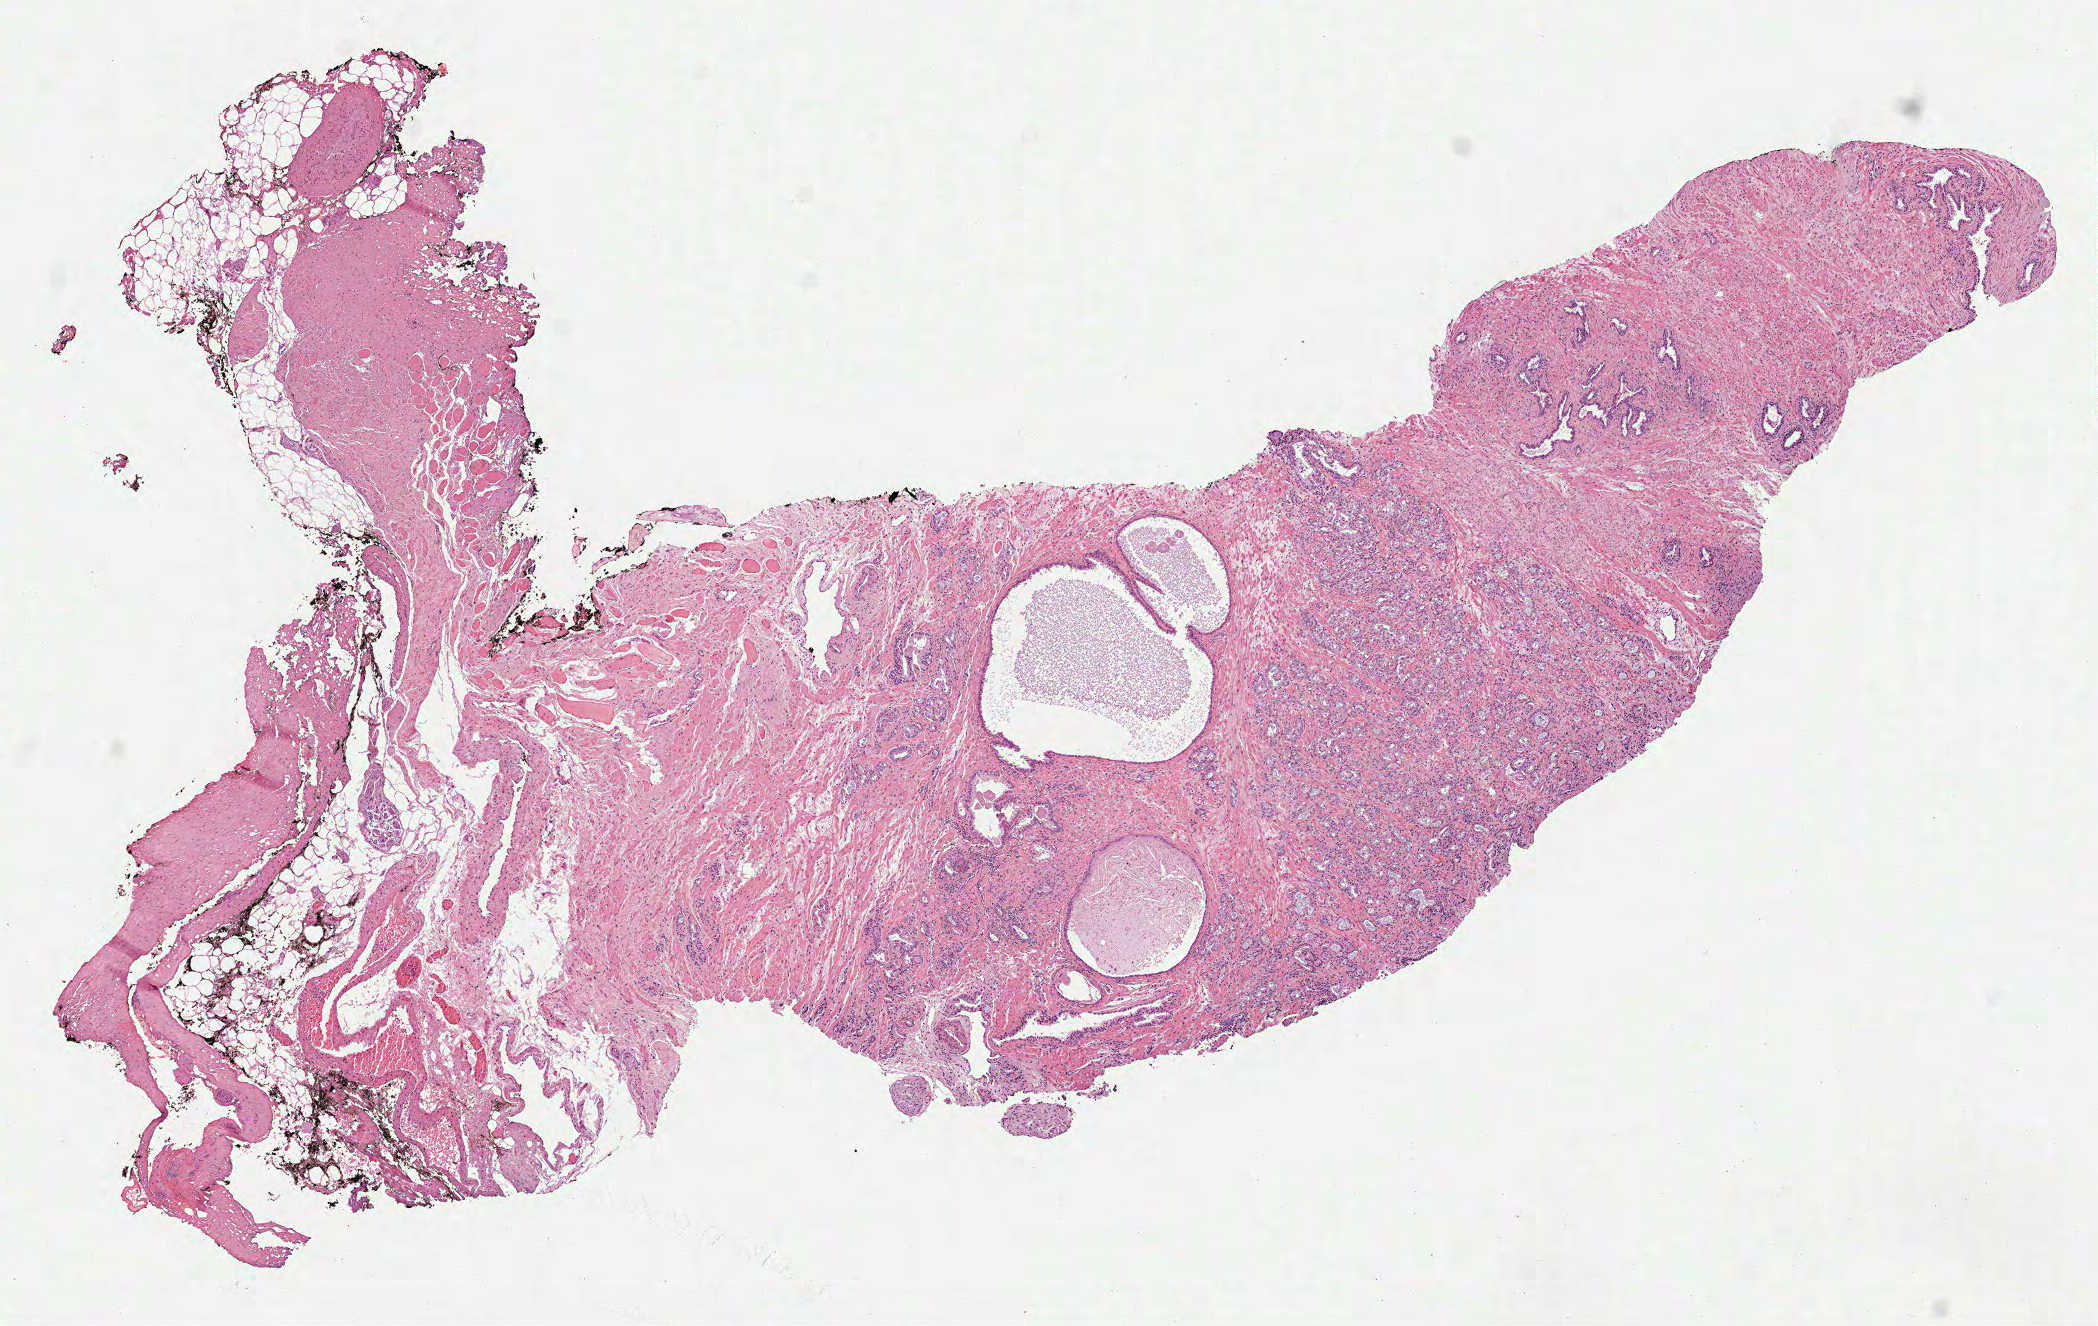
Whole-slide histology image, H&E-stained, low-resolution overview of the scanned area, about 8.5 x 5.3 mm; formalin-fixed paraffin-embedded (FFPE) diagnostic section; sample: primary tumour, prostate. Patient: male, age at initial diagnosis 73 years. Gleason score: 7 (4+3).
Lymph nodes positive (case pathology): 0 of 2 examined. Laterality: left. Pathologic diagnosis: Acinar cell carcinoma (prostate gland).